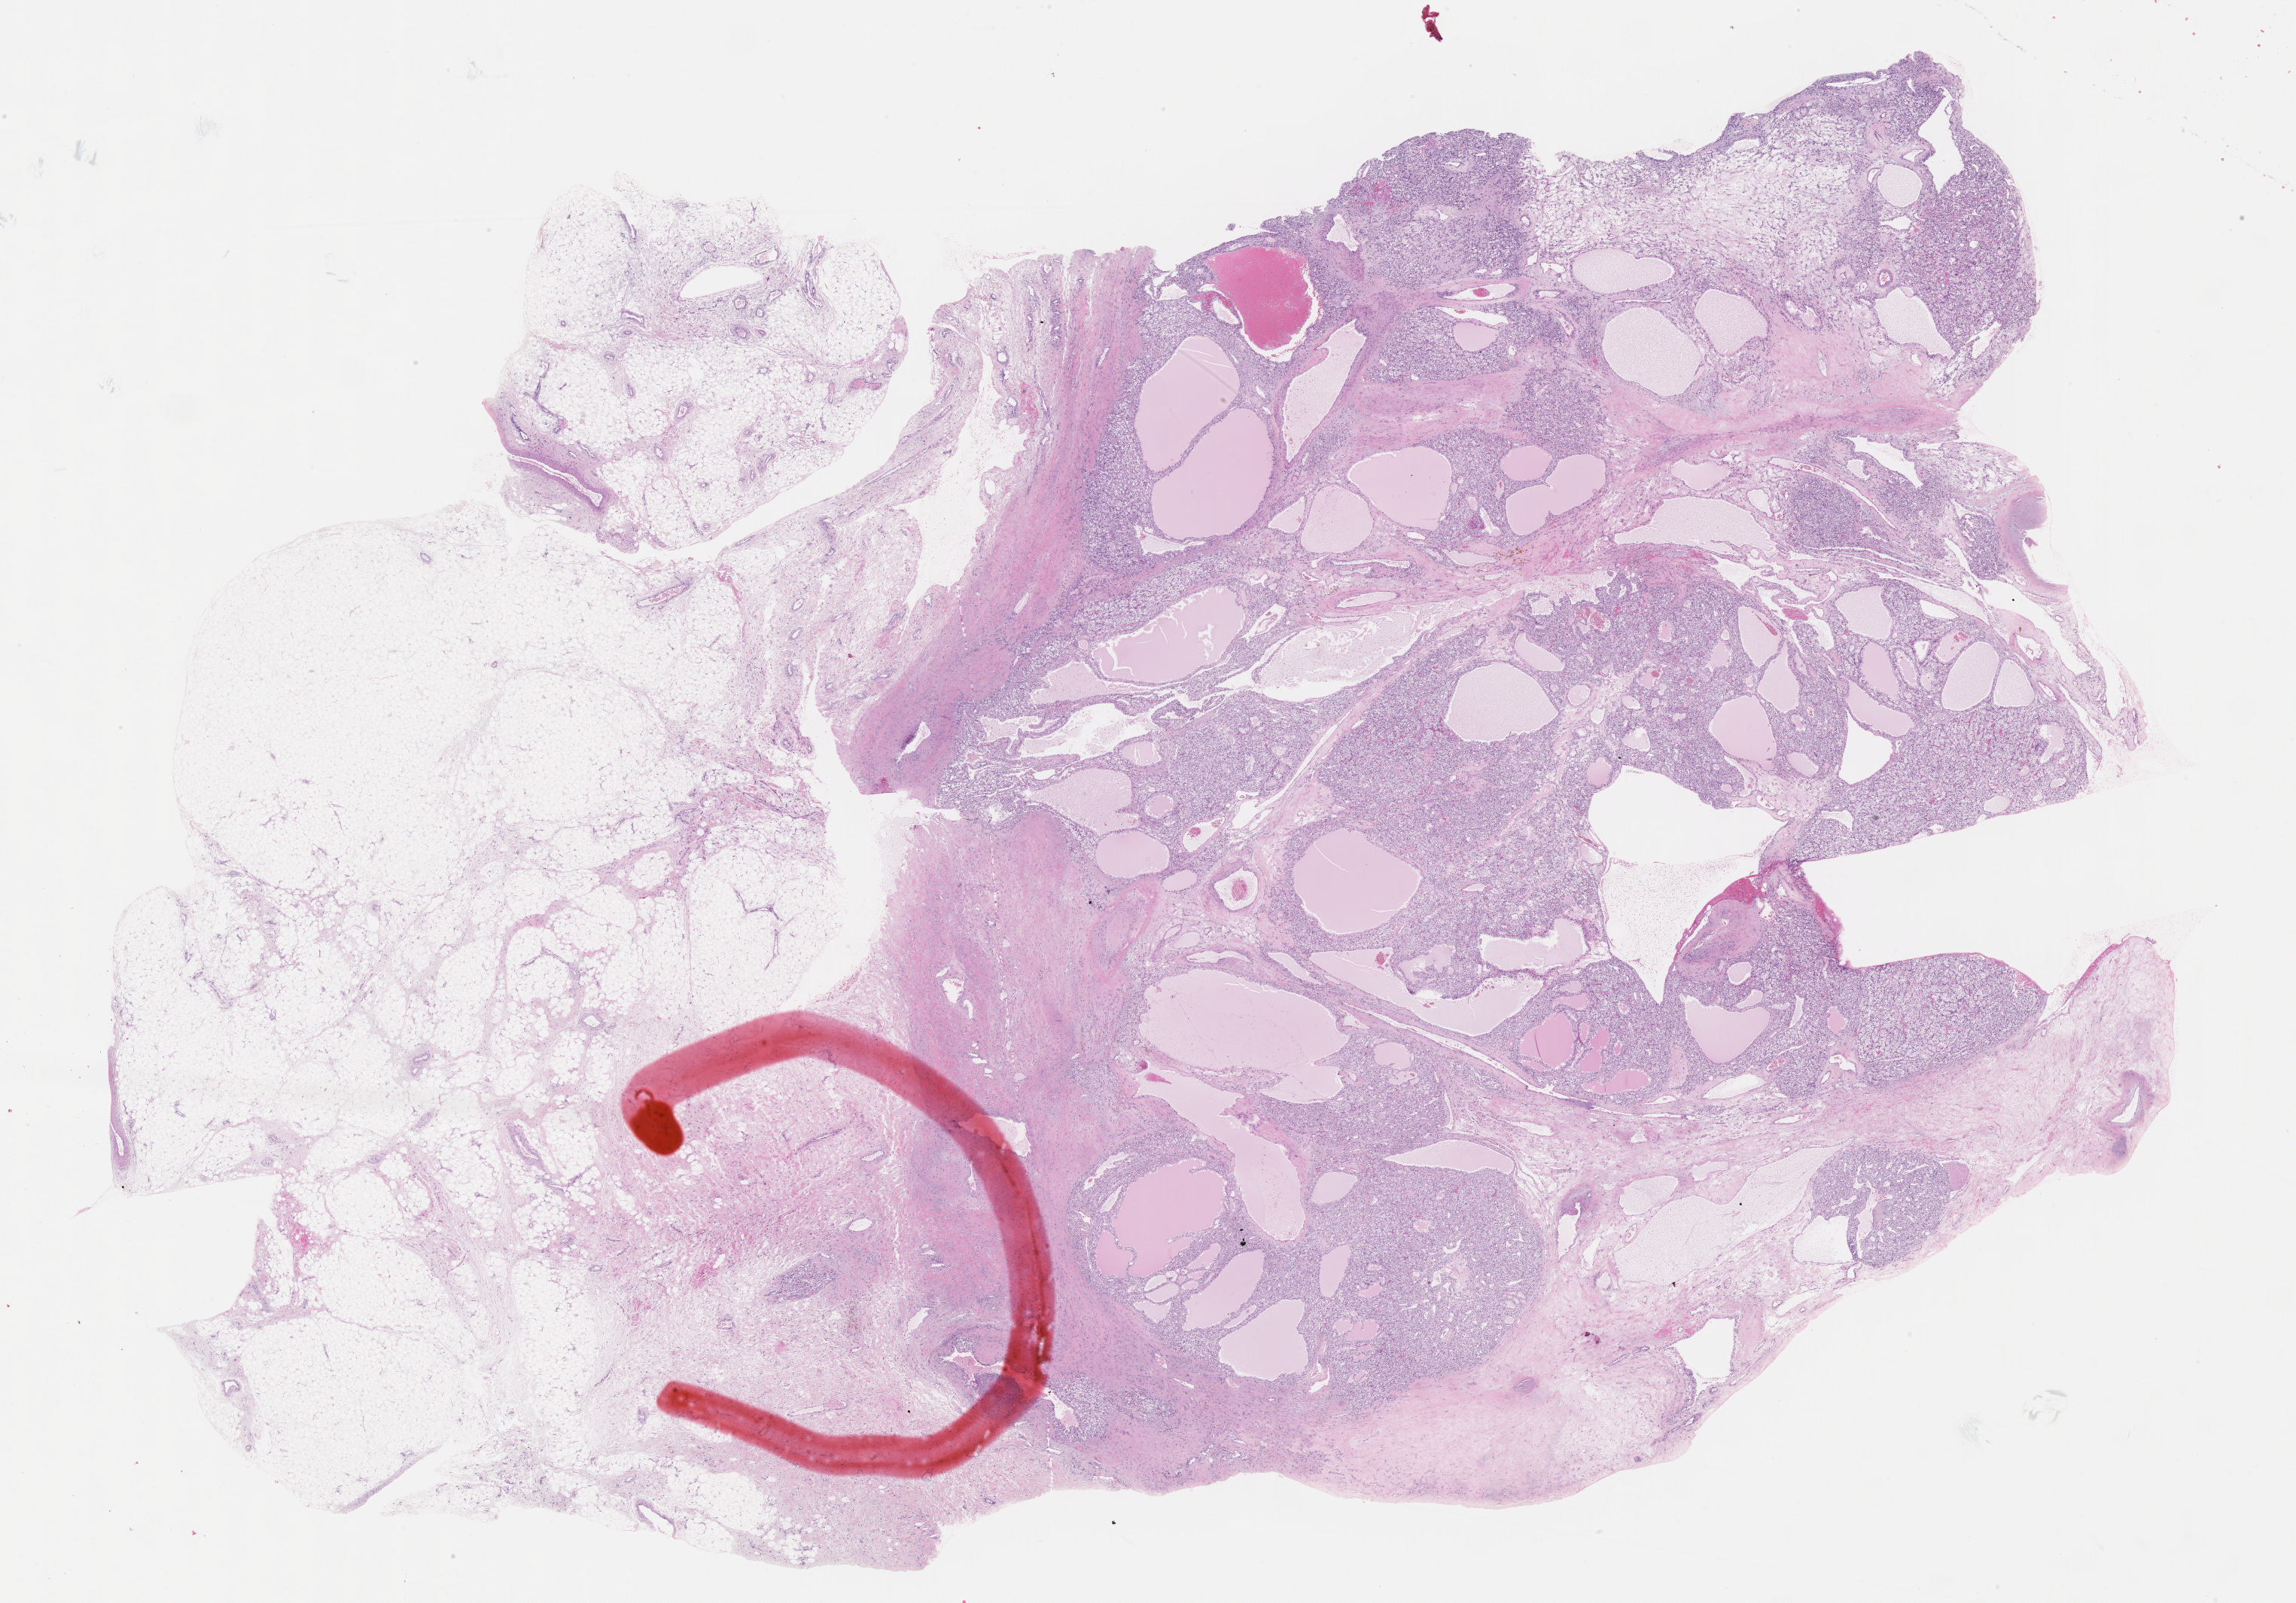
Whole-slide histology image, Hematoxylin and eosin (H&E) stained, low-resolution overview of the scanned area, about 24.7 x 17.2 mm (slide scanned at 40x). Formalin-fixed paraffin-embedded (FFPE) diagnostic section. Sample: primary tumour, kidney. Male patient; age at initial diagnosis 47 years.
Histologic diagnosis: Clear cell adenocarcinoma, NOS.